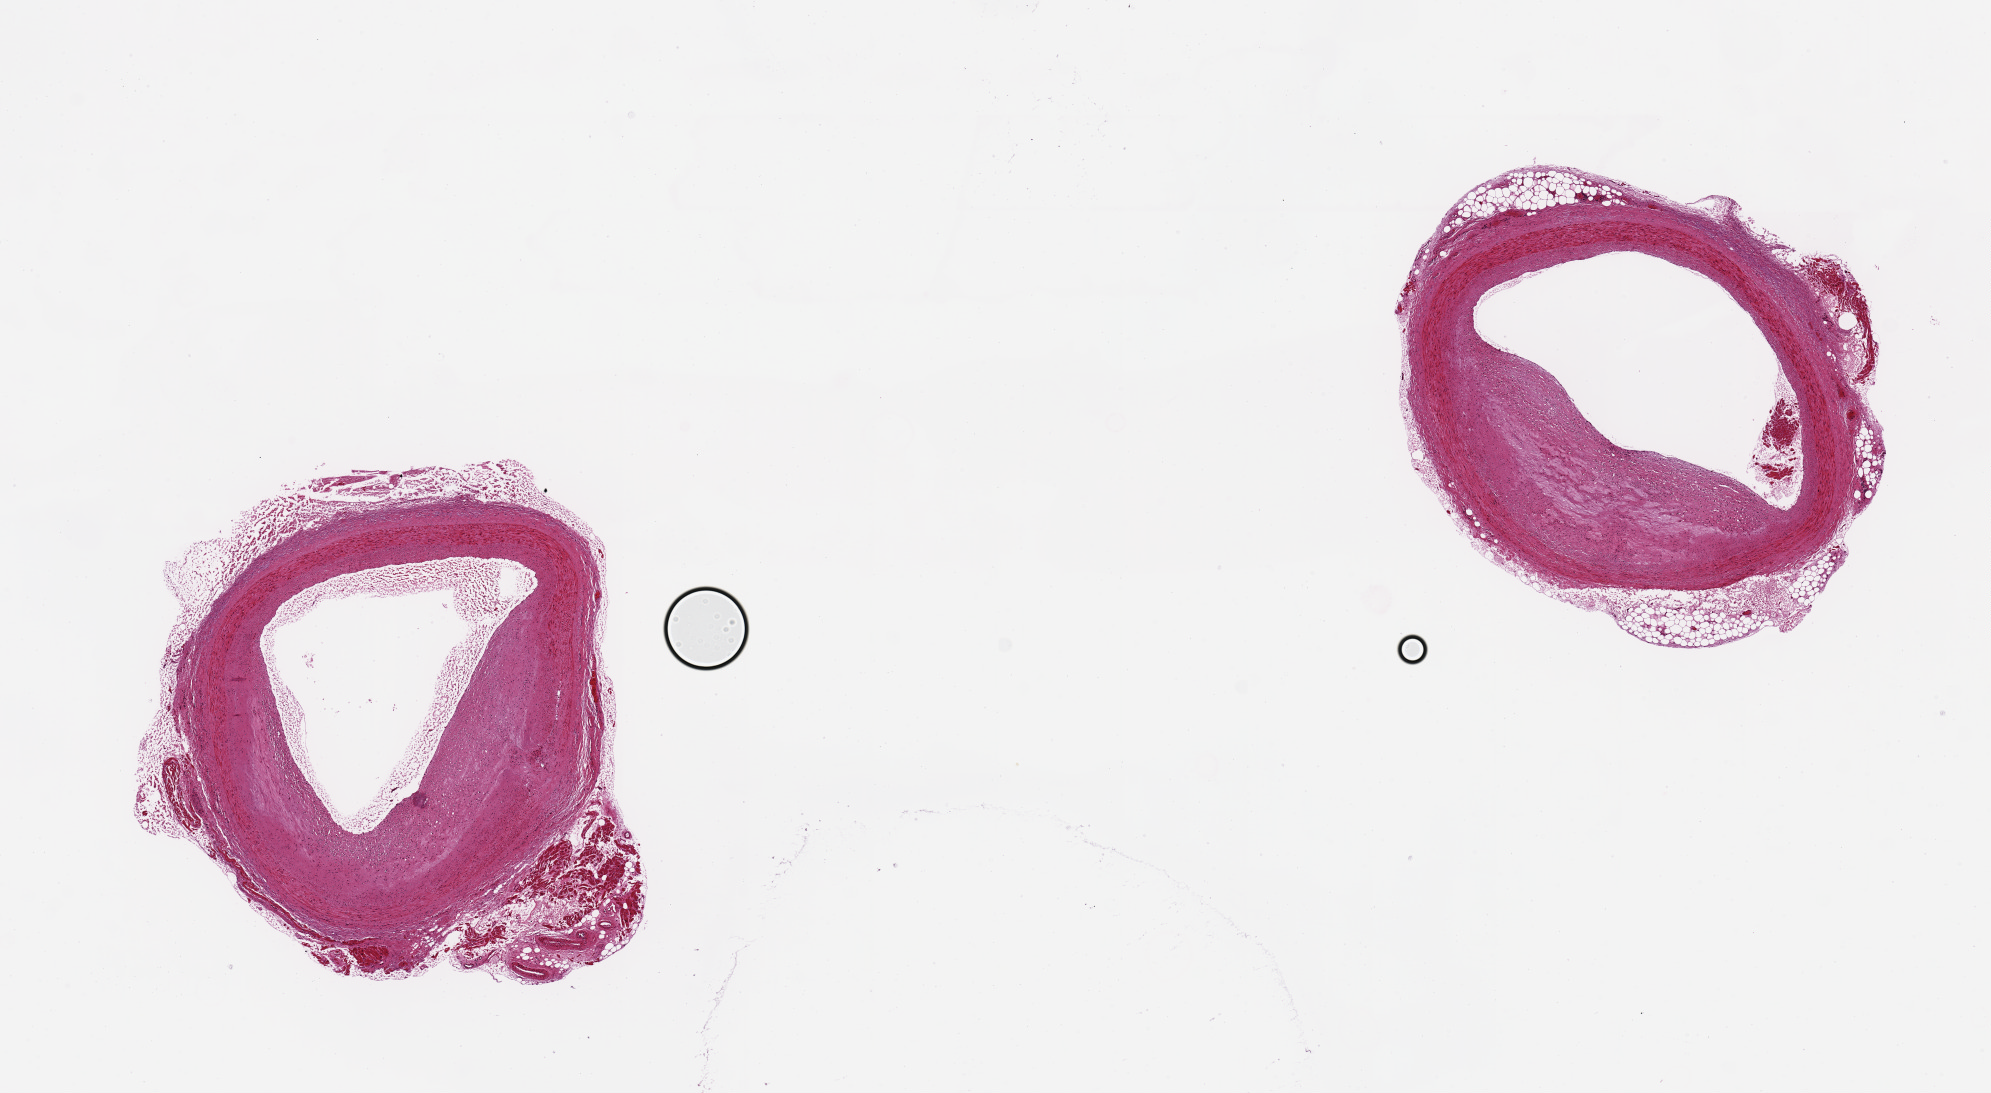
Whole-slide image, H&E stain — low-resolution overview of the scanned area, about 15.8 x 8.6 mm, PAXgene-fixed, paraffin-embedded tissue, target tissue: coronary artery, donor tissue sample. Donor sex: male.
Reviewer comment on this tissue sample: ~40% luminal occlusion by atherosclerotic debris; good clean specimen, minimal peripheral fat/muscle.